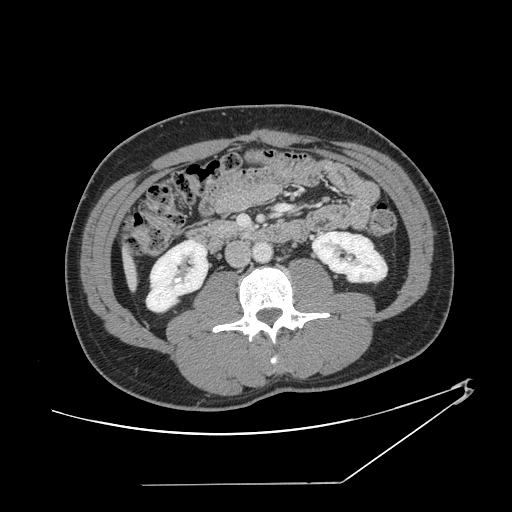
Contrast-enhanced abdominal CT, one axial slice; position 40 of 152 along the scan axis; soft-tissue window (W 400 / L 40 HU); 2.5 mm slice thickness; 512 × 512 image matrix, field of view 432 × 432 mm. Male patient, age 45 years. From the clinical record (not read from this slice): diagnosis: colorectal cancer liver metastases, imaged before liver resection.
Annotated regions visible in this slice (outlined manually by an expert reader):
- liver: bounding box <127,258,135,284> (left, top, right, bottom; pixels)
- planned liver remnant (the part of the liver to remain after resection): <126,257,135,284>